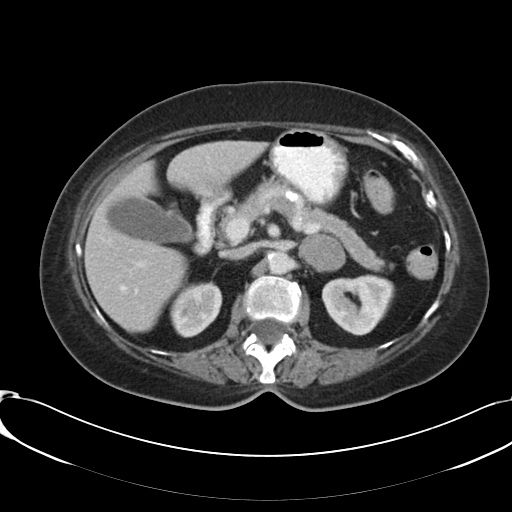
Contrast-enhanced abdominal CT, one axial slice; position 67 of 91 along the scan axis; reconstruction kernel B30f; intravenous contrast given; soft-tissue window (W 400 / L 40 HU); 5 mm slice thickness; 512 × 512 image matrix, field of view 366 × 366 mm. Patient: female, 73 years. From the clinical record (not read from this slice): diagnosis: adrenocortical carcinoma; tumour side: left adrenal.
Outlined on this slice (semi-automatically segmented with operator editing):
- mass: box from (x=300, y=235) to (x=345, y=271) px